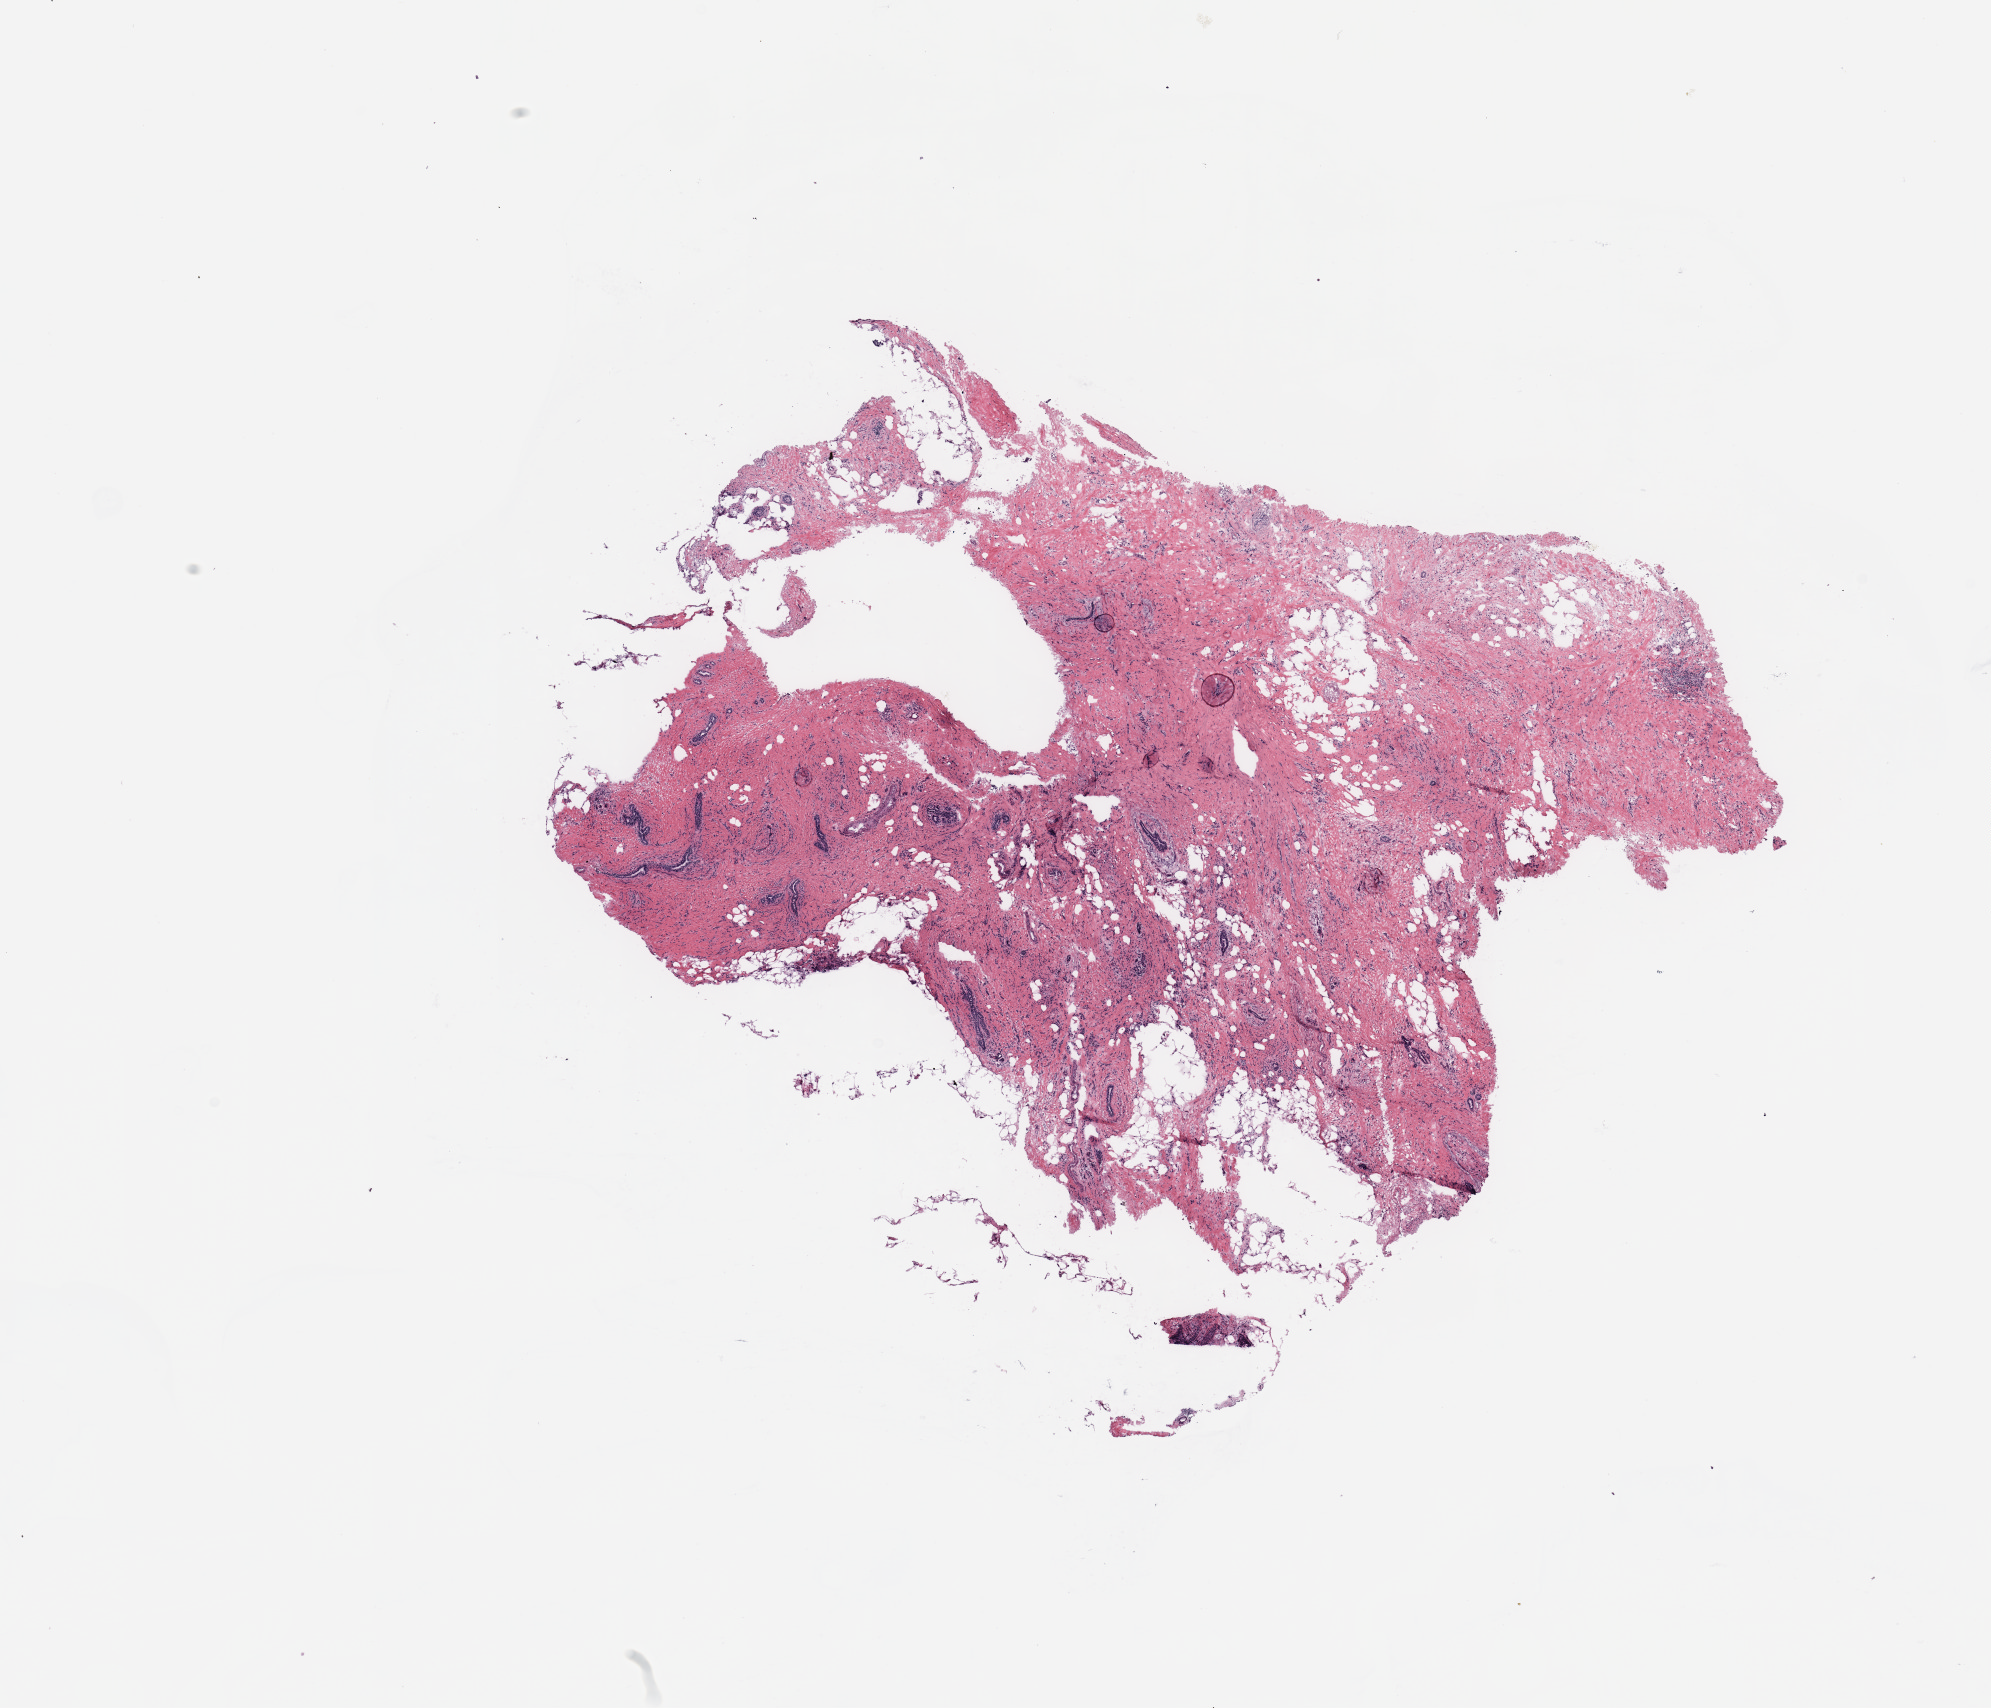
Whole-slide histology image, H&E, low-resolution overview of the scanned area, about 15.8 x 13.5 mm (acquisition: 20x scan); breast, tissue type not recorded.
• patient diagnosis (cohort enrolment): breast cancer (breast)